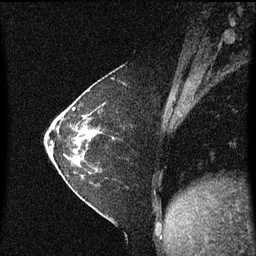
Breast MRI (dynamic contrast-enhanced), one sagittal slice. Position 20 of 60 along the scan axis. Dynamic contrast-enhanced series, image 2 of 3 at this slice position (ordered by acquisition). 1.5 T. TE 4.2 ms, TR 8.4 ms. 256 × 256 image matrix, field of view 200 × 200 mm. Female patient, age 36 years. Case-level facts recorded for this patient, not image findings: setting: breast cancer imaged before/during neoadjuvant chemotherapy; receptor status: HR-positive, HER2-negative.
Outlined on this slice (semi-automatically segmented with operator editing):
- analysis volume of interest (the breast-tissue region the enhancement analysis was run in; not a lesion): bounding box [x1, y1, x2, y2] px = [66, 102, 123, 179]
- tumour enhancement mask (voxels above the 70 % enhancement threshold inside the analysis volume of interest): [78, 130, 91, 141]